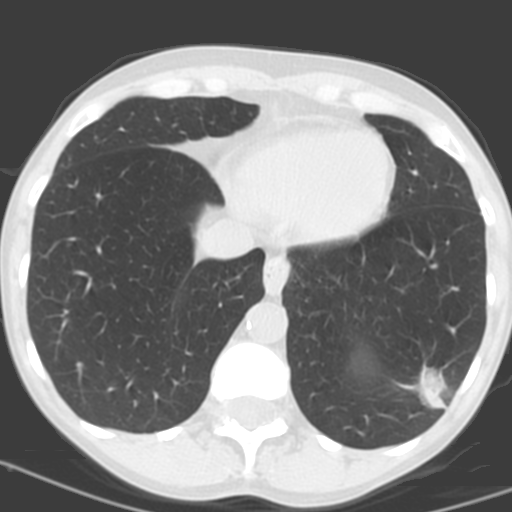
Chest CT (low-dose screening protocol), one axial image, first (baseline) screen, lung window (W 1500 / L -600 HU), 3.2 mm slice thickness, slice 114 of 156 in the series, 512 × 512 image matrix, field of view 262 × 262 mm. Female participant, aged 56 years at enrolment. Current smoker at enrolment.
• Expert reader's lesion annotation, box from (x=394, y=355) to (x=469, y=423) px.
• Screening reader's record for this exam (one nodule recorded; not confirmed to be the boxed lesion): non-calcified nodule or mass ≥4 mm, left lower lobe, 31 × 23 mm, poorly defined margins, soft tissue attenuation, pre-existing on the prior screen: no.
• Official screen result: positive, change unspecified: nodule(s) >= 4 mm or enlarging nodule(s), mass(es), or other non-specific abnormalities suspicious for lung cancer.
• Lung cancer was diagnosed 27 days after this screen: squamous cell carcinoma, NOS, left lower lobe, poorly differentiated (G3), stage IB (AJCC 6th edition), 35 mm at pathology.